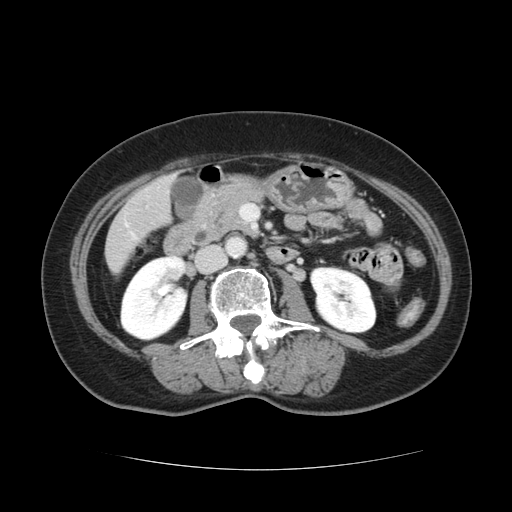
Contrast-enhanced abdominal CT, one axial slice. Position 32 of 128 along the scan axis. 120 kVp. Intravenous contrast given. Soft-tissue window (W 400 / L 40 HU). 2.5 mm slice thickness. 512 × 512 image matrix, field of view 366 × 366 mm. Female patient, age 67 years. From the clinical record (not read from this slice): diagnosis: colorectal cancer liver metastases, imaged before liver resection; multiple liver metastases: yes; largest metastasis: 3 cm; disease in both lobes: yes.
Annotated regions visible in this slice (manually delineated by an expert):
- liver: bounding box (x1, y1, x2, y2) in pixels: (105, 178, 172, 271)
- planned liver remnant (the part of the liver to remain after resection): (105, 214, 139, 271)